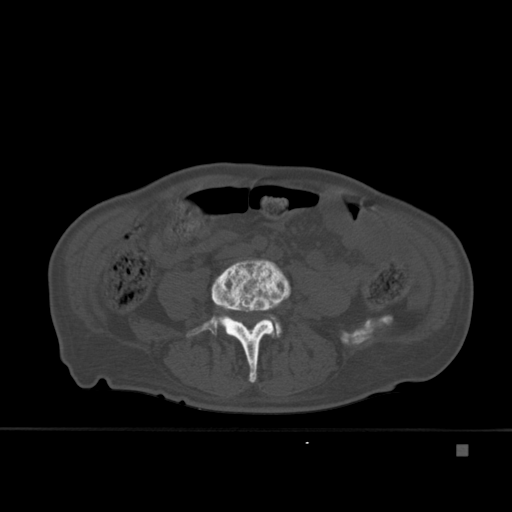
CT including the spine, one axial slice. Position 120 of 451 along the scan axis. Bone window (W 1800 / L 400 HU). 512 × 512 image matrix, field of view 378 × 378 mm. Patient: male, 75 years. From the clinical record (not read from this slice): primary cancer: prostate.
Outlined on this slice (semi-automatically segmented with operator editing):
- L4 vertebra: bounding box (x1, y1, x2, y2) in pixels: (186, 259, 291, 383)
- L5 vertebra: (269, 314, 282, 338)